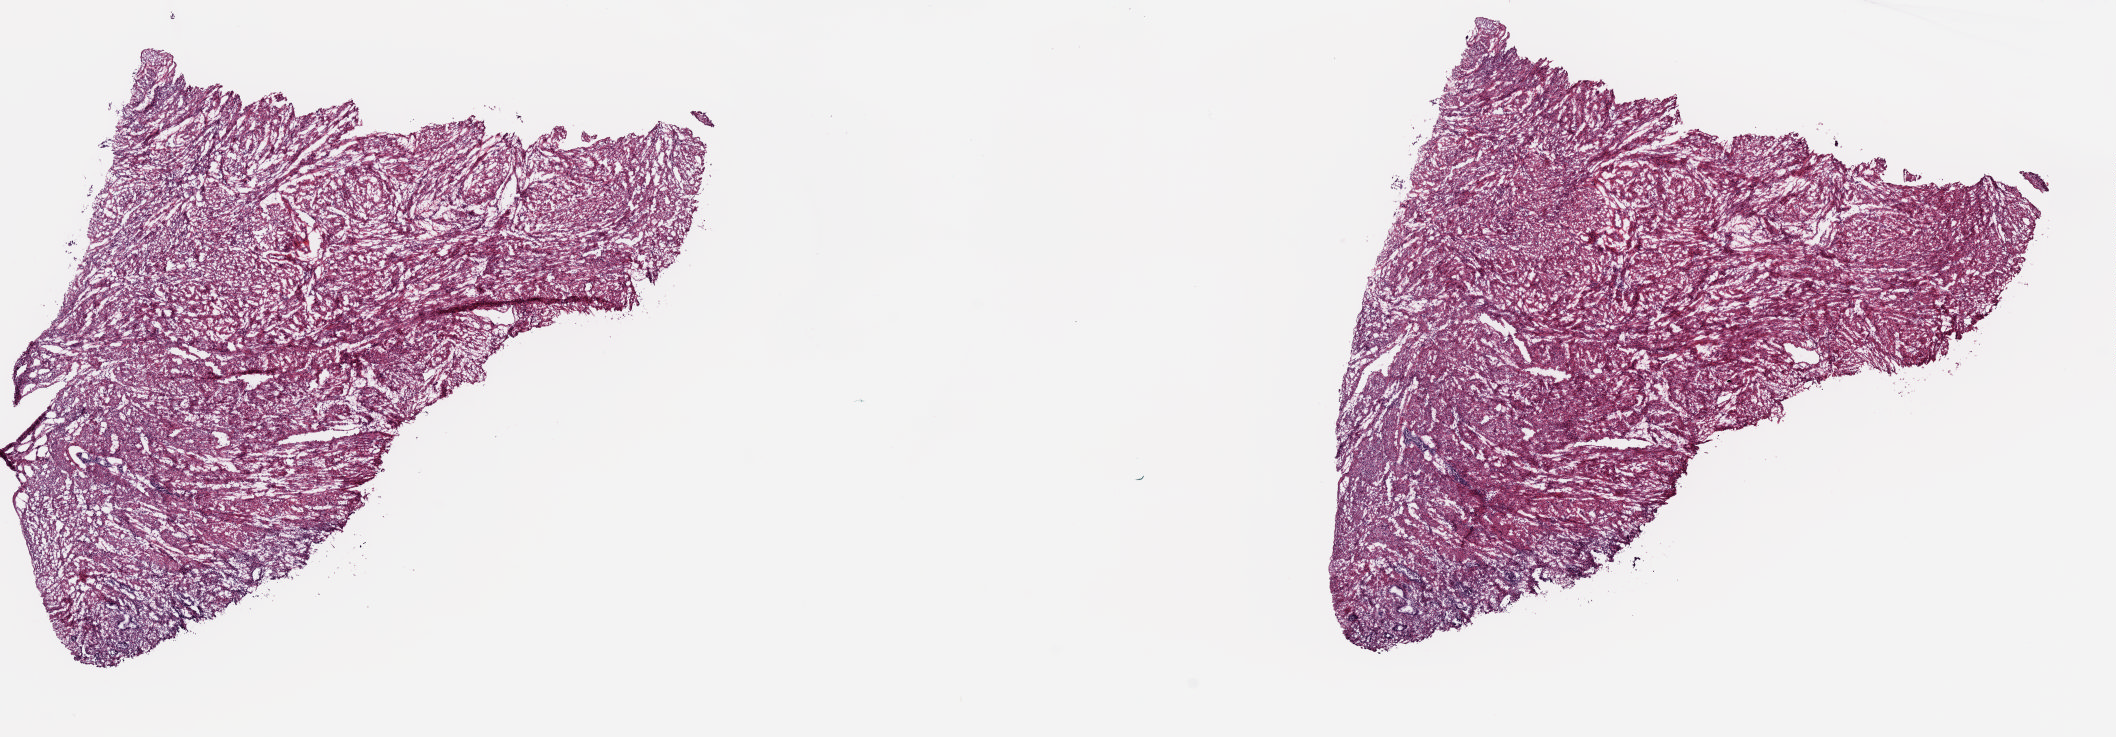
Digitized Hematoxylin and eosin (H&E) stained tissue section (whole slide), shown as a low-resolution overview of the whole scanned area (about 16.7 x 5.8 mm, acquisition: 20x scan), frozen section from the top of the tissue portion, sample: solid tissue normal (non-tumour tissue), uterus. Female patient; age at initial diagnosis 47 years. Pathologist review of this section (percent, as recorded): tumour cells 0%, tumour nuclei 0%, normal cells 100%, stromal cells 0%, necrosis 0%. Infiltration values recorded for this section: lymphocyte infiltration 0%, monocyte infiltration 0%, neutrophil infiltration 0%.
- this section: solid tissue normal (non-tumour) sample from the same patient
- patient diagnosis: Endometrioid adenocarcinoma, NOS (endometrium)